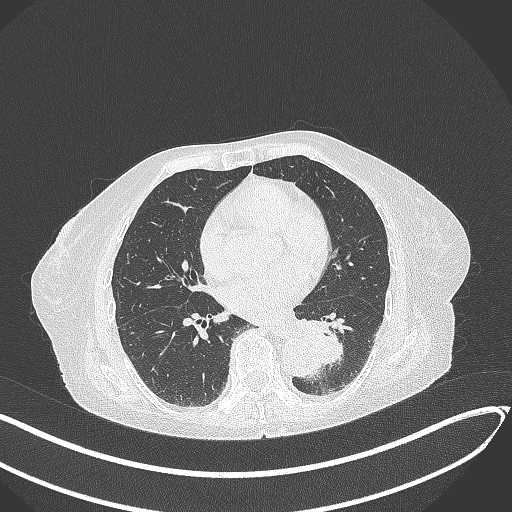
Chest CT, one axial slice; reconstruction kernel B70f; lung window (W 1500 / L -600 HU); 1 mm slice thickness; 512 × 512 image matrix, field of view 400 × 400 mm. Female patient, age 82 years. Case-level facts recorded for this patient, not image findings: clinical TNM (as recorded): T1b N0 M1.
Structures marked on this image (bounding box drawn by a radiologist):
- lung tumour (recorded histology: adenocarcinoma): bounding box (x1, y1, x2, y2) in pixels: (294, 314, 351, 368)